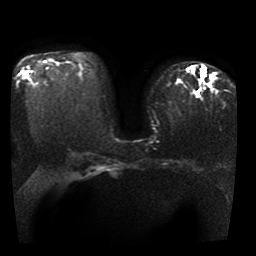
Breast MRI, one axial slice; slice 24 of 41 in the series (ordered by position); diffusion-weighted series; image 2 of 4 stored at this slice position (different b-values; order by instance number); 1.5 T; 5 mm slice thickness; 256 × 256 image matrix. Female patient.
Structures marked on this image (outlined manually by an expert reader):
- tumour on diffusion-weighted imaging: bounding box (x1, y1, x2, y2) in pixels: (190, 66, 204, 83)